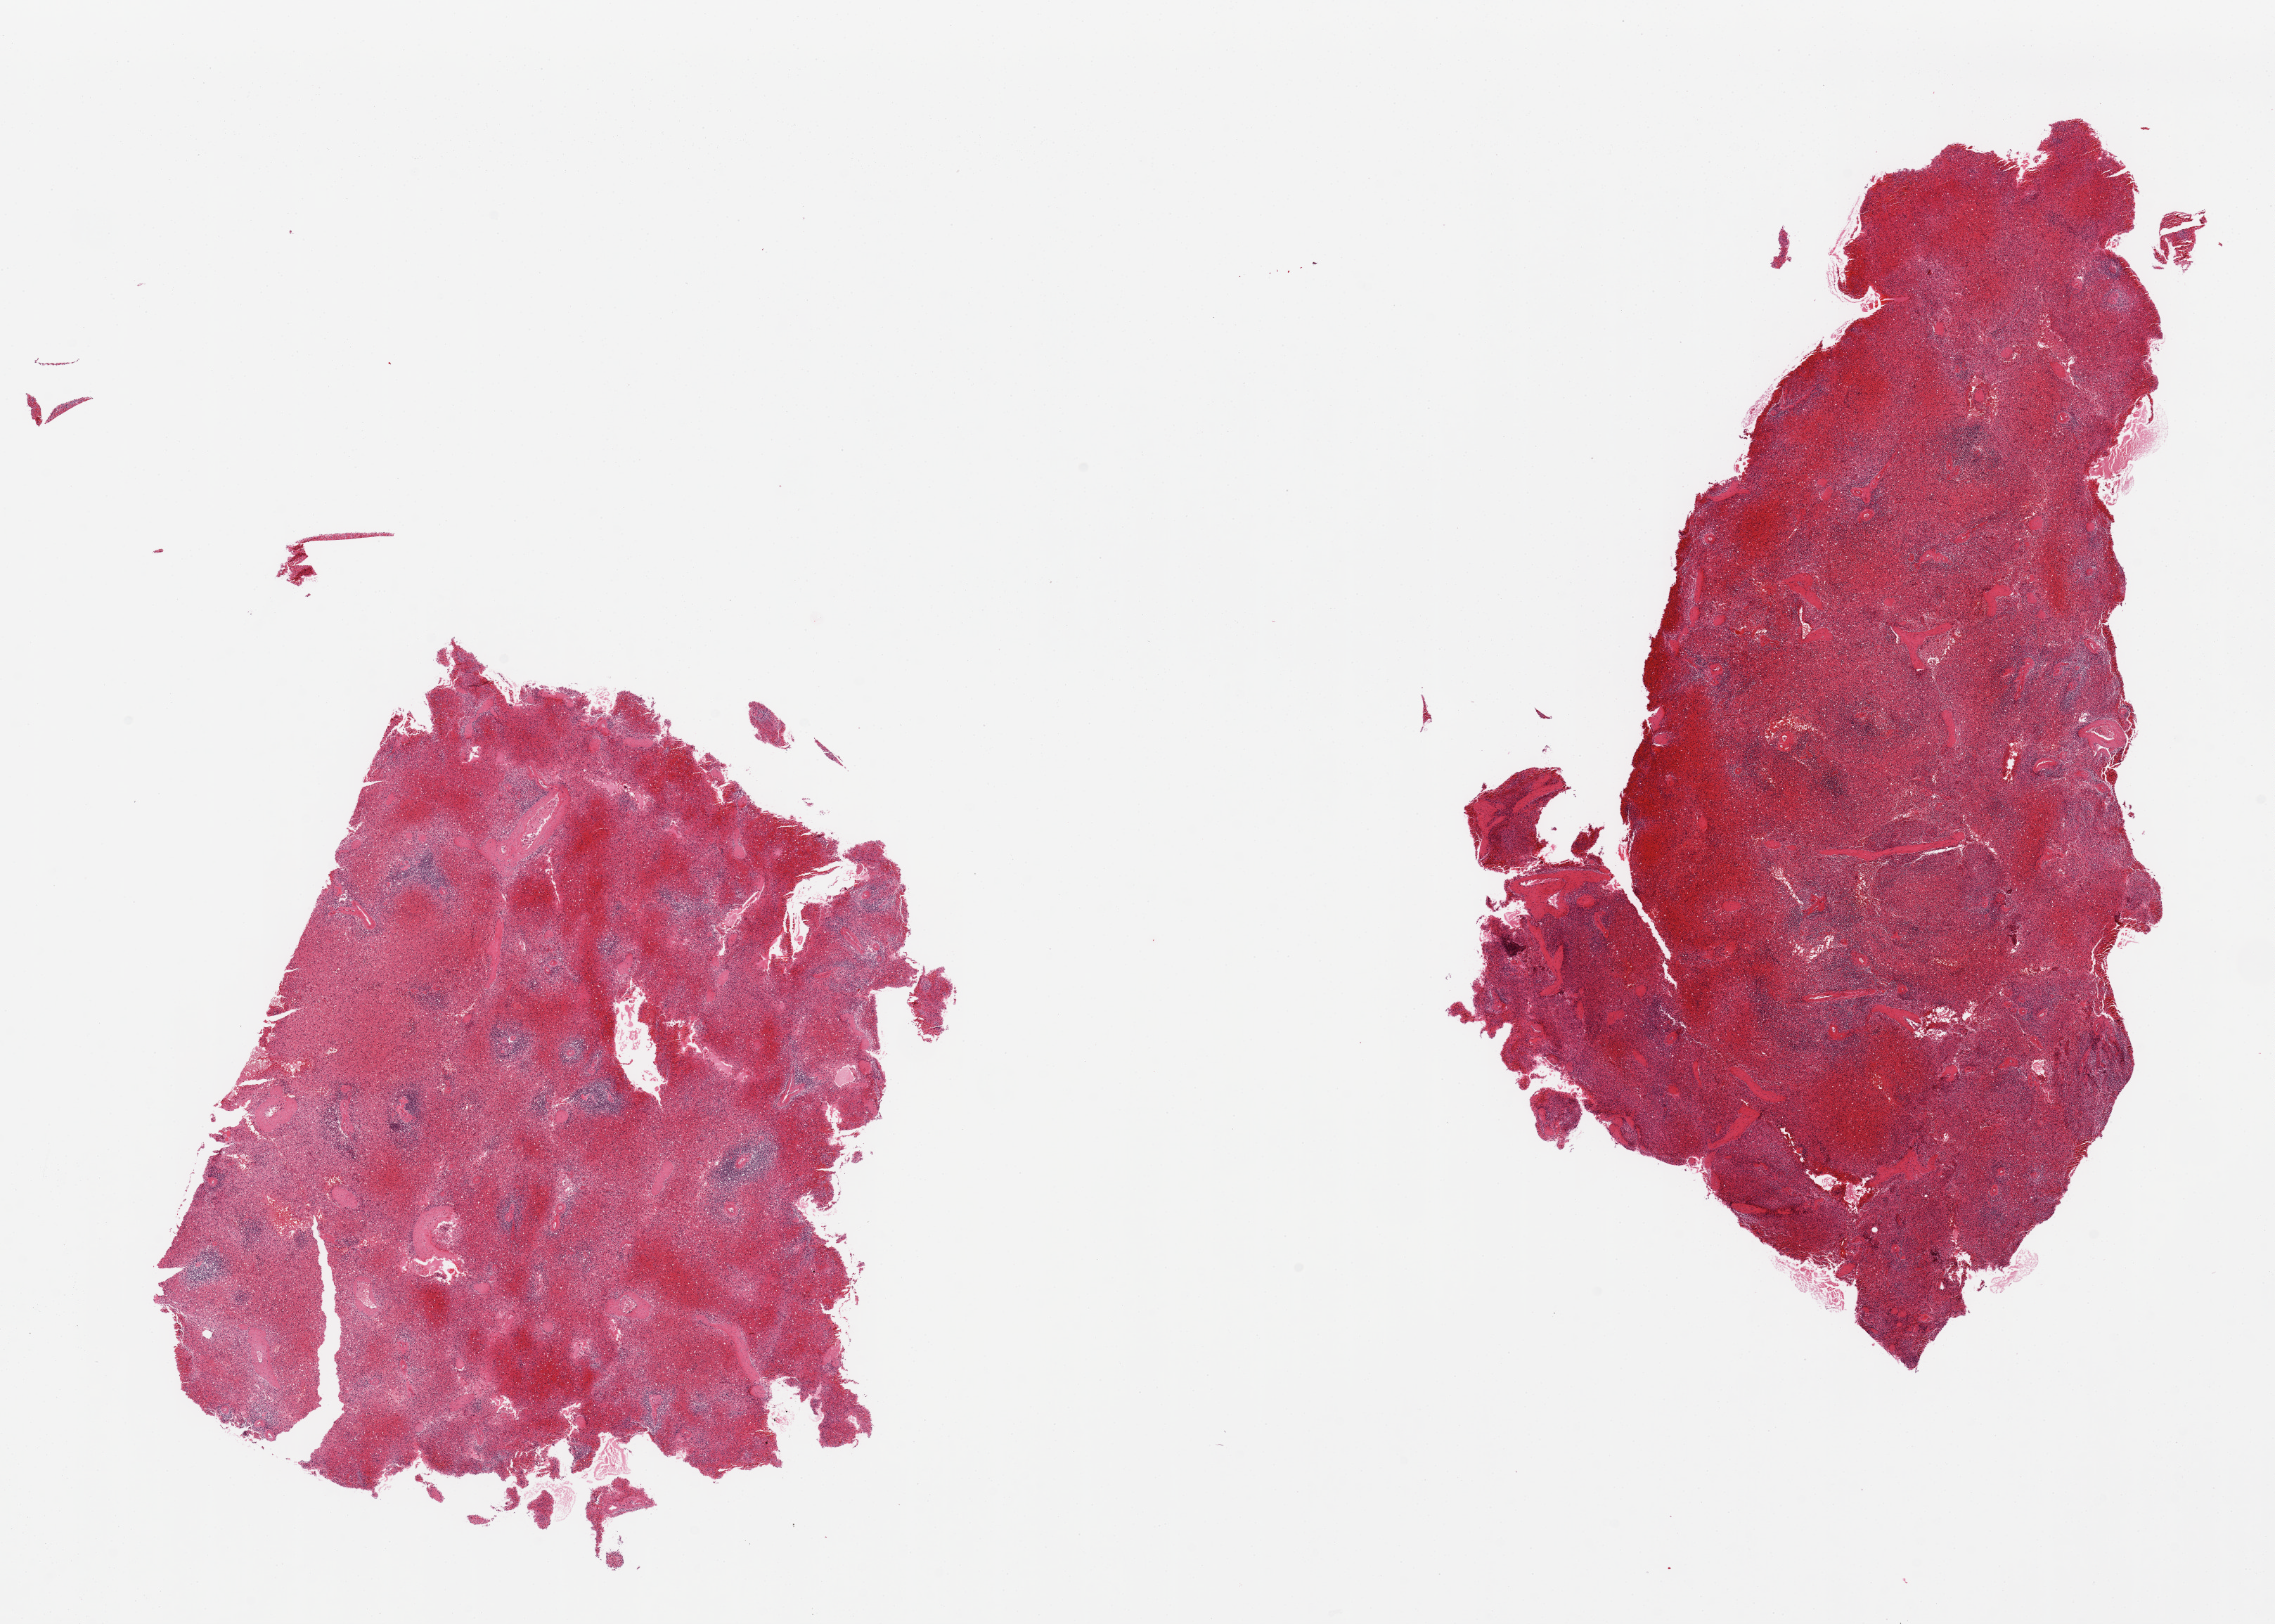
Whole-slide image, hematoxylin and eosin (H&E) stain — a low-resolution overview of the entire scanned area, about 25.6 x 18.3 mm; PAXgene-fixed paraffin-embedded (PFPE) section; target tissue: spleen; donor tissue sample.
Pathologist's review note for this sample: 2 pieces; congested.